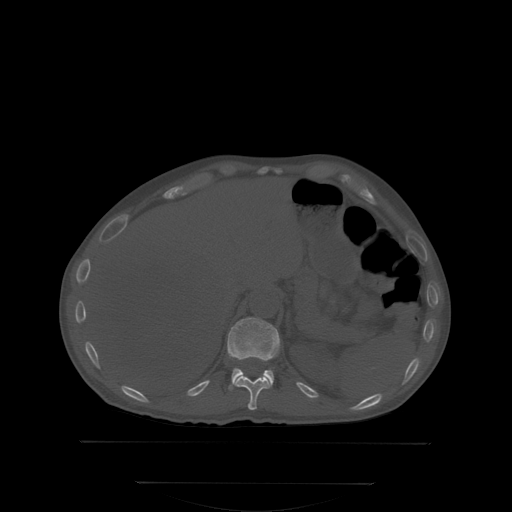
CT including the spine, one axial slice; slice 175 of 350 in the series (ordered by position); bone window (W 1800 / L 400 HU); 2.5 mm slice thickness; 512 × 512 image matrix, field of view 500 × 500 mm. Male patient, age 58 years. Case-level facts recorded for this patient, not image findings: primary cancer: prostate; vertebrae with lytic lesions (as recorded): L1.
Structures marked on this image (semi-automatic segmentation, software-assisted and operator-edited):
- T11 vertebra: bounding box [x1, y1, x2, y2] px = [236, 351, 278, 410]
- T12 vertebra: [228, 317, 280, 388]